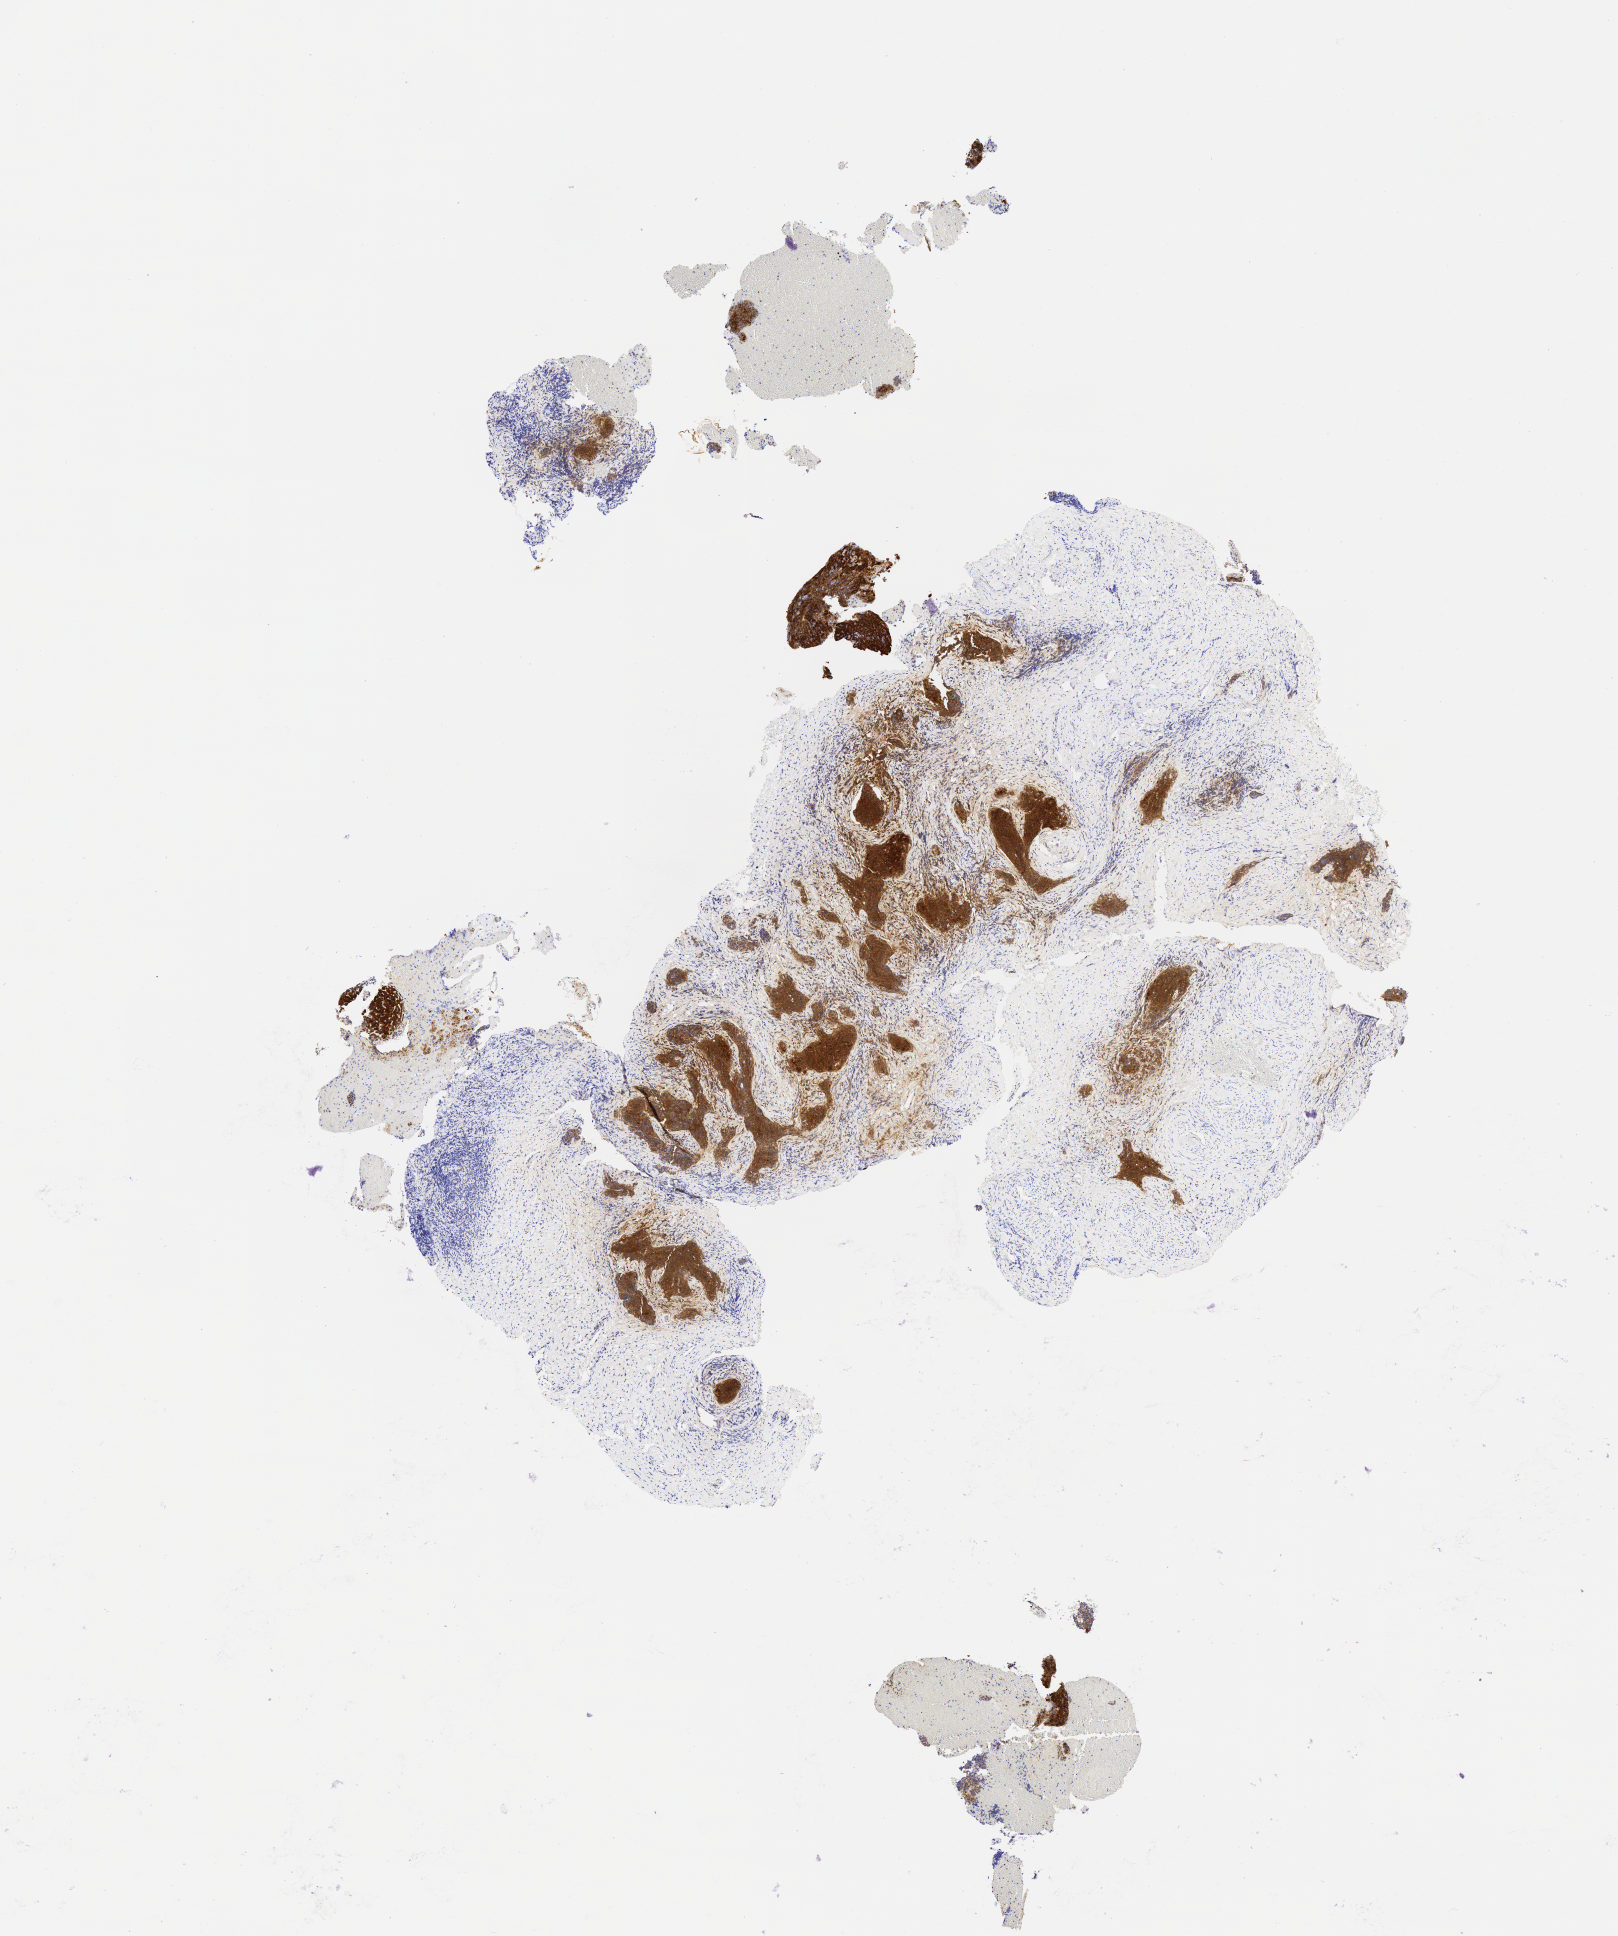
IHC for p16 (p16INK4a), whole-slide image, low-resolution overview of the scanned area, about 6.5 x 7.8 mm; specimen: tumor tissue; anatomic site: cervix. Patient: female, aged 58.
Histologic diagnosis: Squamous cell carcinoma, large cell, nonkeratinizing, NOS.